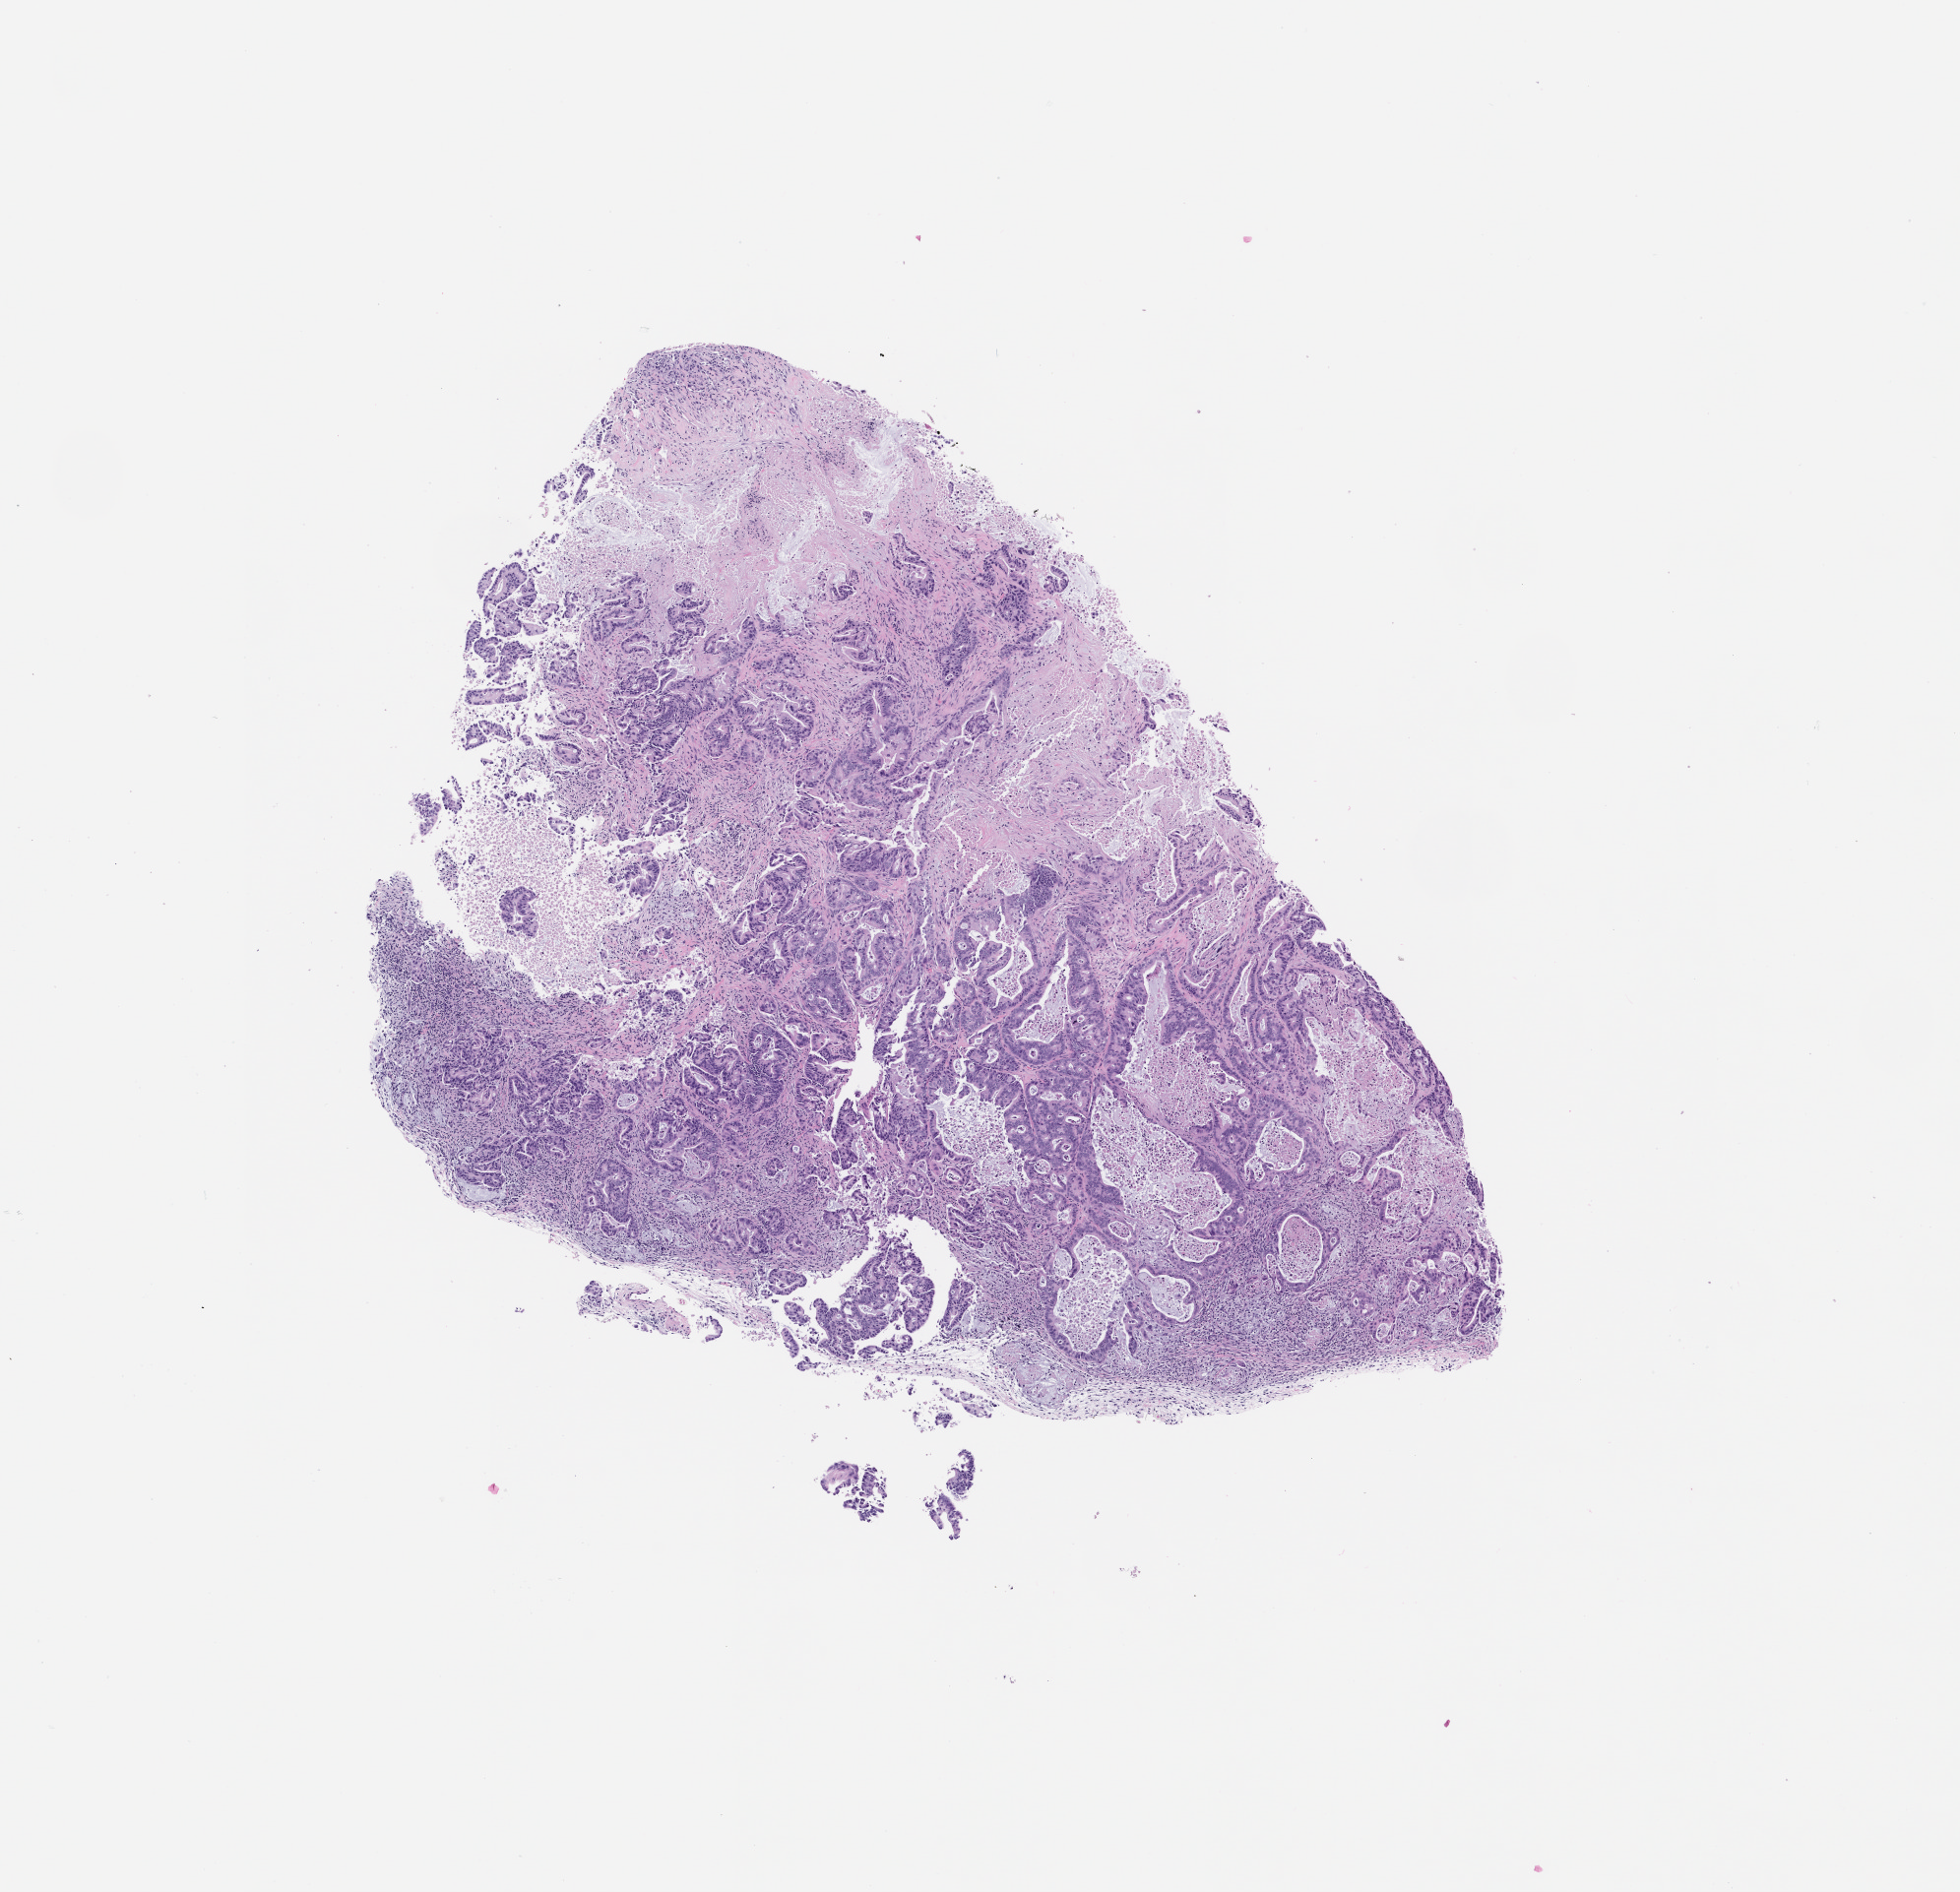
Whole-slide image, haematoxylin and eosin: patient-derived xenograft (human tumor grown in a mouse), passage 0 — shown as a low-resolution overview of the whole scanned area (about 8.0 x 7.7 mm). Formalin-fixed paraffin-embedded section. Originating tumor site category: pancreas.
Originating patient diagnosis: Pancreatic Adenocarcinoma.